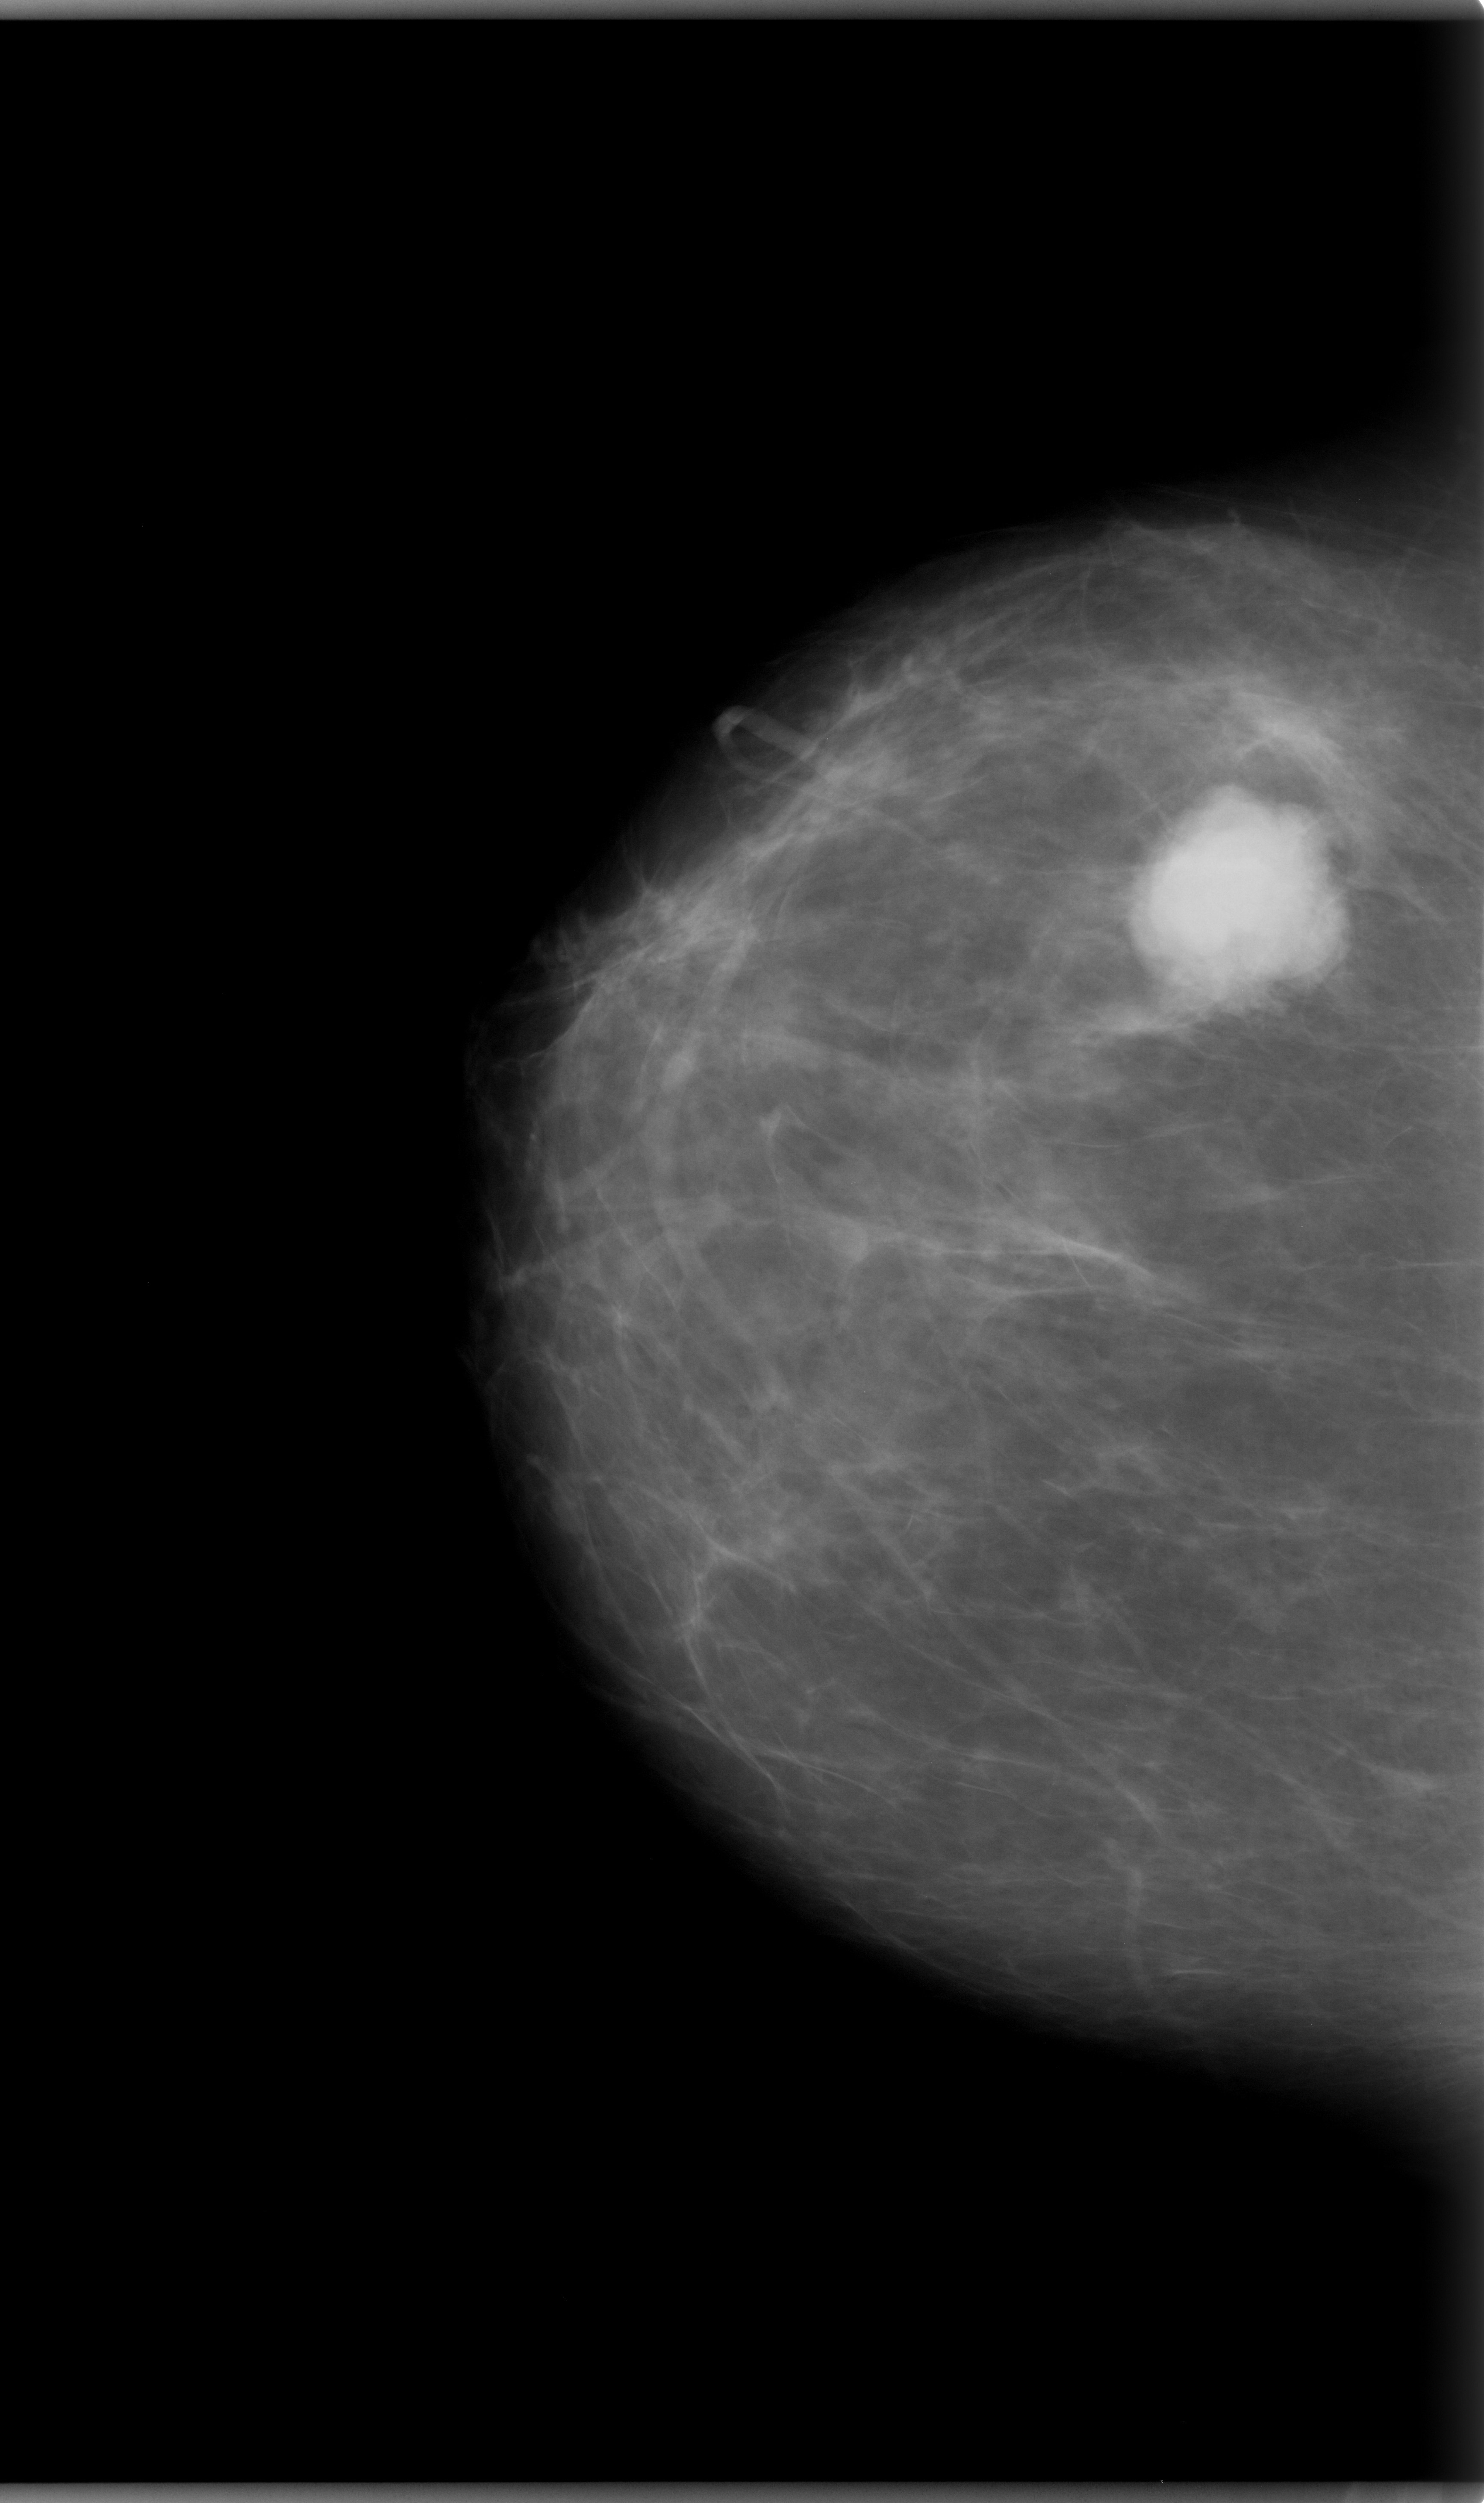
Mammogram (digitized film); right breast; craniocaudal (CC) view; BI-RADS breast density category 1 (scale 1–4); 1484 × 2503 image matrix.
Expert-marked regions of interest on this film, with their recorded descriptors:
- mass, shape lobulated, margins microlobulated; BI-RADS assessment category 5; subtlety rating 5 on a 1 (subtle) to 5 (obvious) scale; pathology result (as recorded, not read from the image): malignant: bounding box <1128,800,1344,1003> (left, top, right, bottom; pixels)